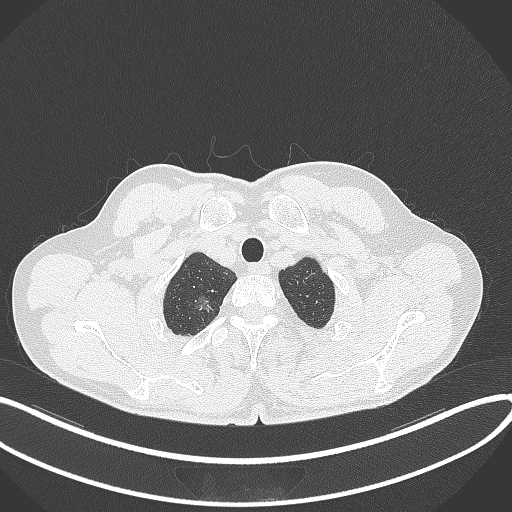
Chest CT, one axial slice; slice 353 of 407 in the series (ordered by position); reconstruction kernel B70f; lung window (W 1500 / L -600 HU); 512 × 512 image matrix. Patient: male, 58 years. From the clinical record (not read from this slice): clinical TNM (as recorded): T1c N0 M0; histopathological grade: G1-2.
Structures marked on this image (bounding box drawn by a radiologist):
- lung tumour (recorded histology: adenocarcinoma): bounding box (x1, y1, x2, y2) in pixels: (192, 291, 215, 319)